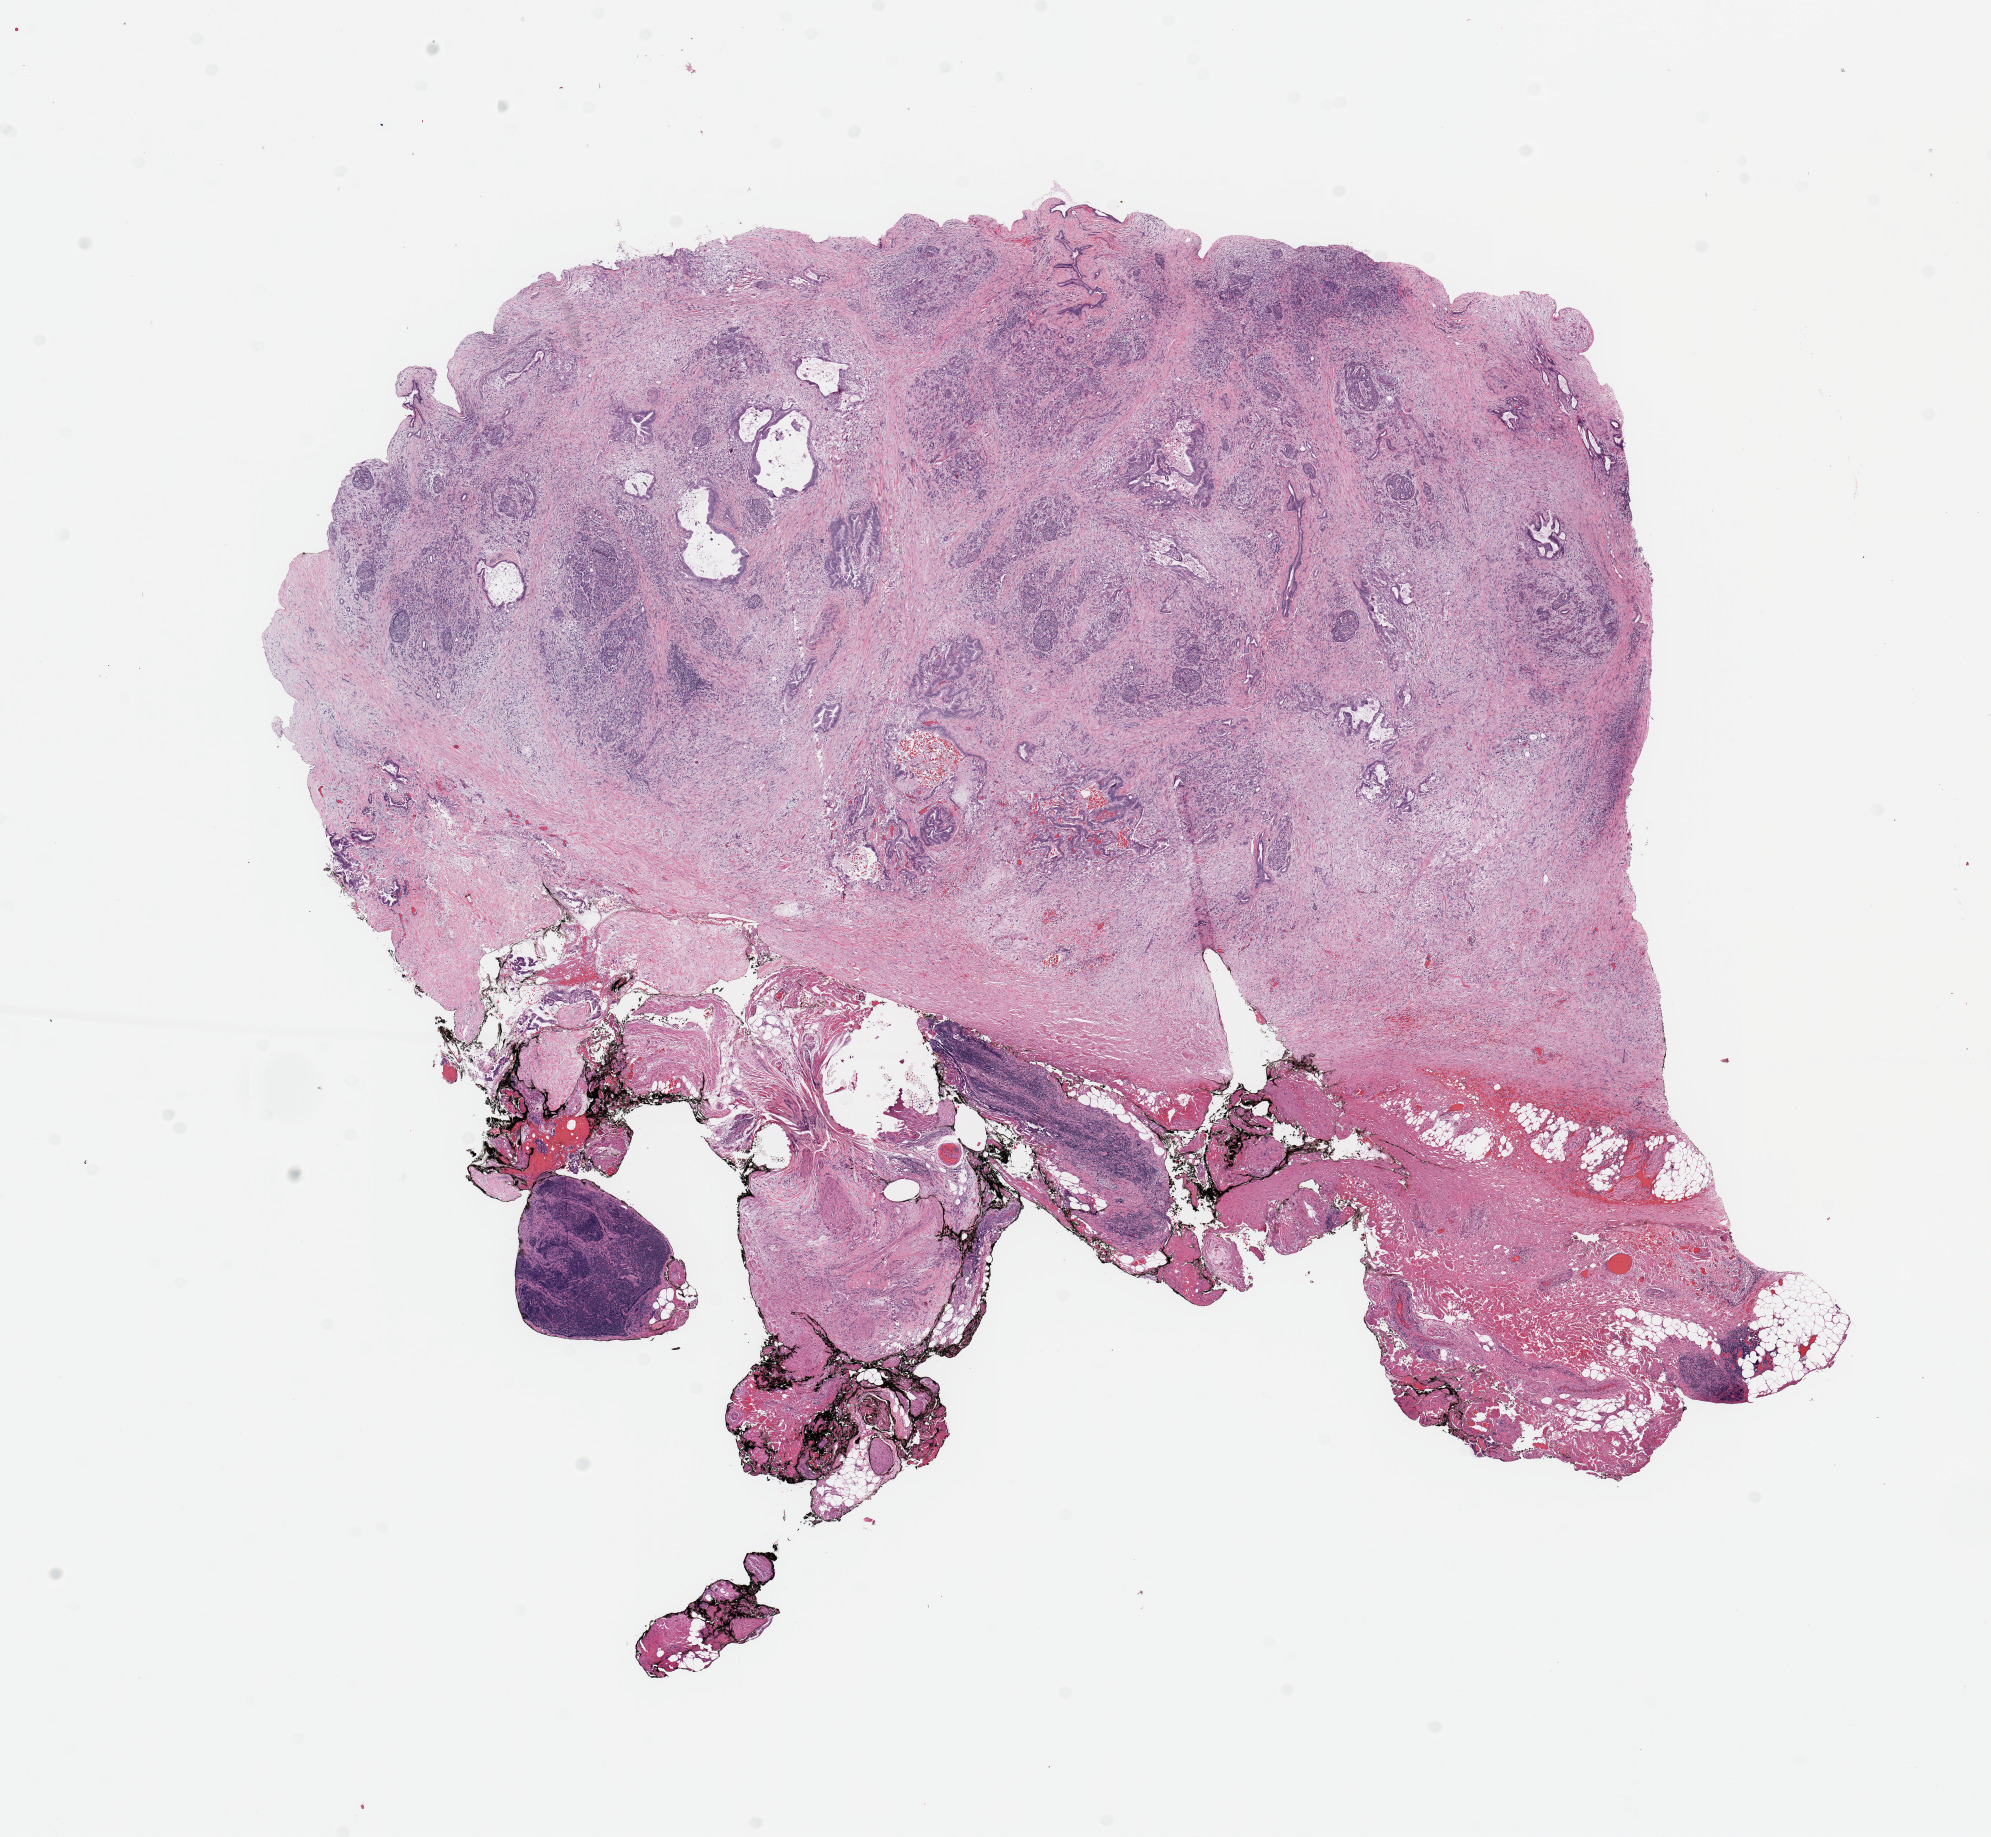
H&E-stained whole-slide image — low-resolution overview of the scanned area, about 15.8 x 14.5 mm, tumour tissue sample, pancreas. Patient: female, age 38 years. Histologic grade: G2 (moderately differentiated).
* primary tumour site (as recorded): head
* diagnosis: Infiltrating duct carcinoma, NOS
* AJCC pathologic stage: IV